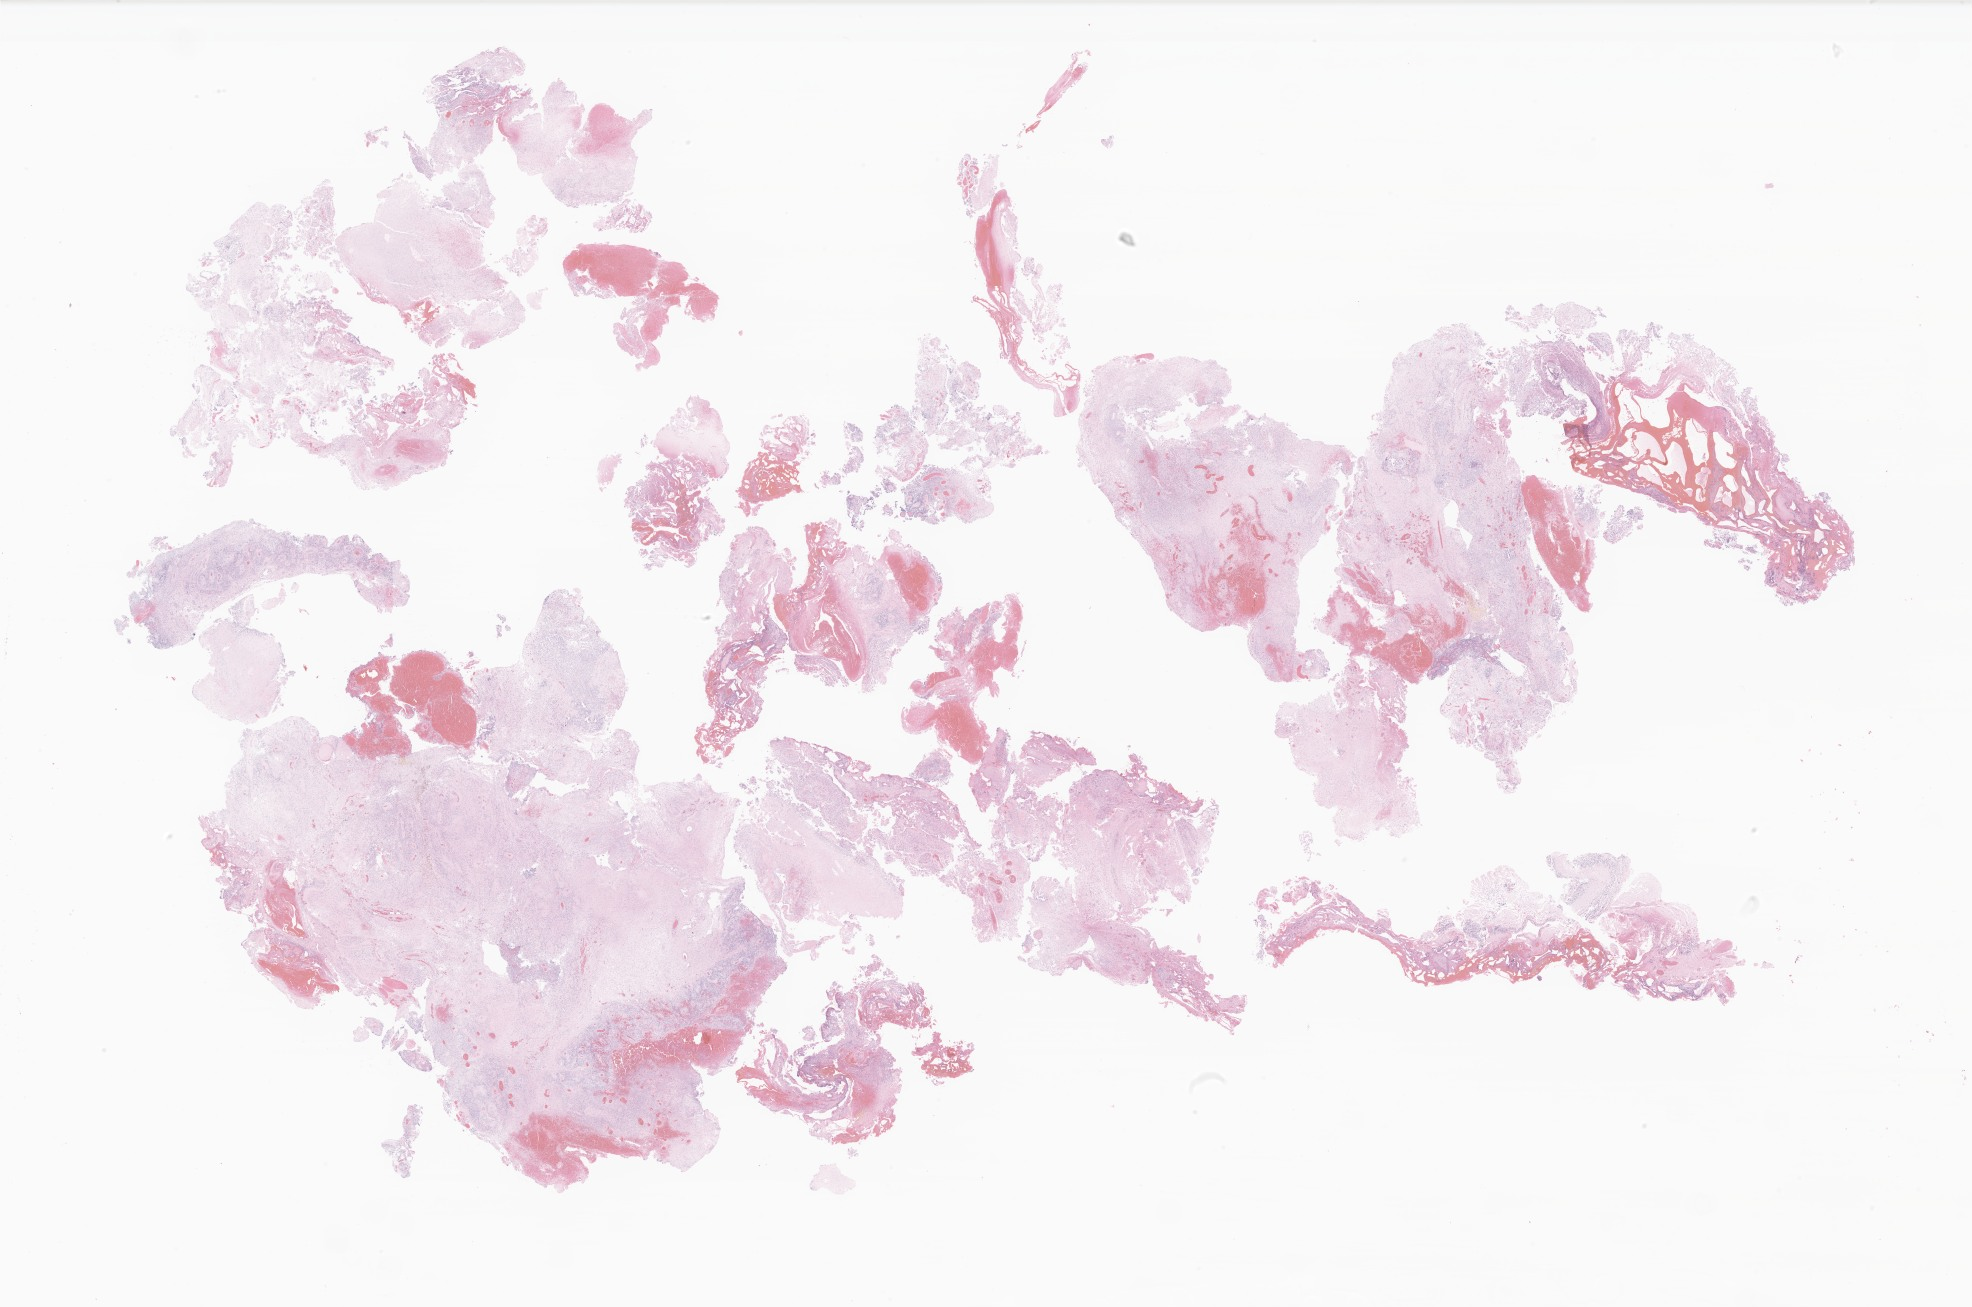
Whole-slide image, H&E stain of tumor tissue from the brain — whole scanned area (about 33.3 x 22.0 mm) shown as a low-resolution overview. FFPE section. Male patient, age 545 days (about 1.5 years).
Diagnosis: Ependymoma, NOS.